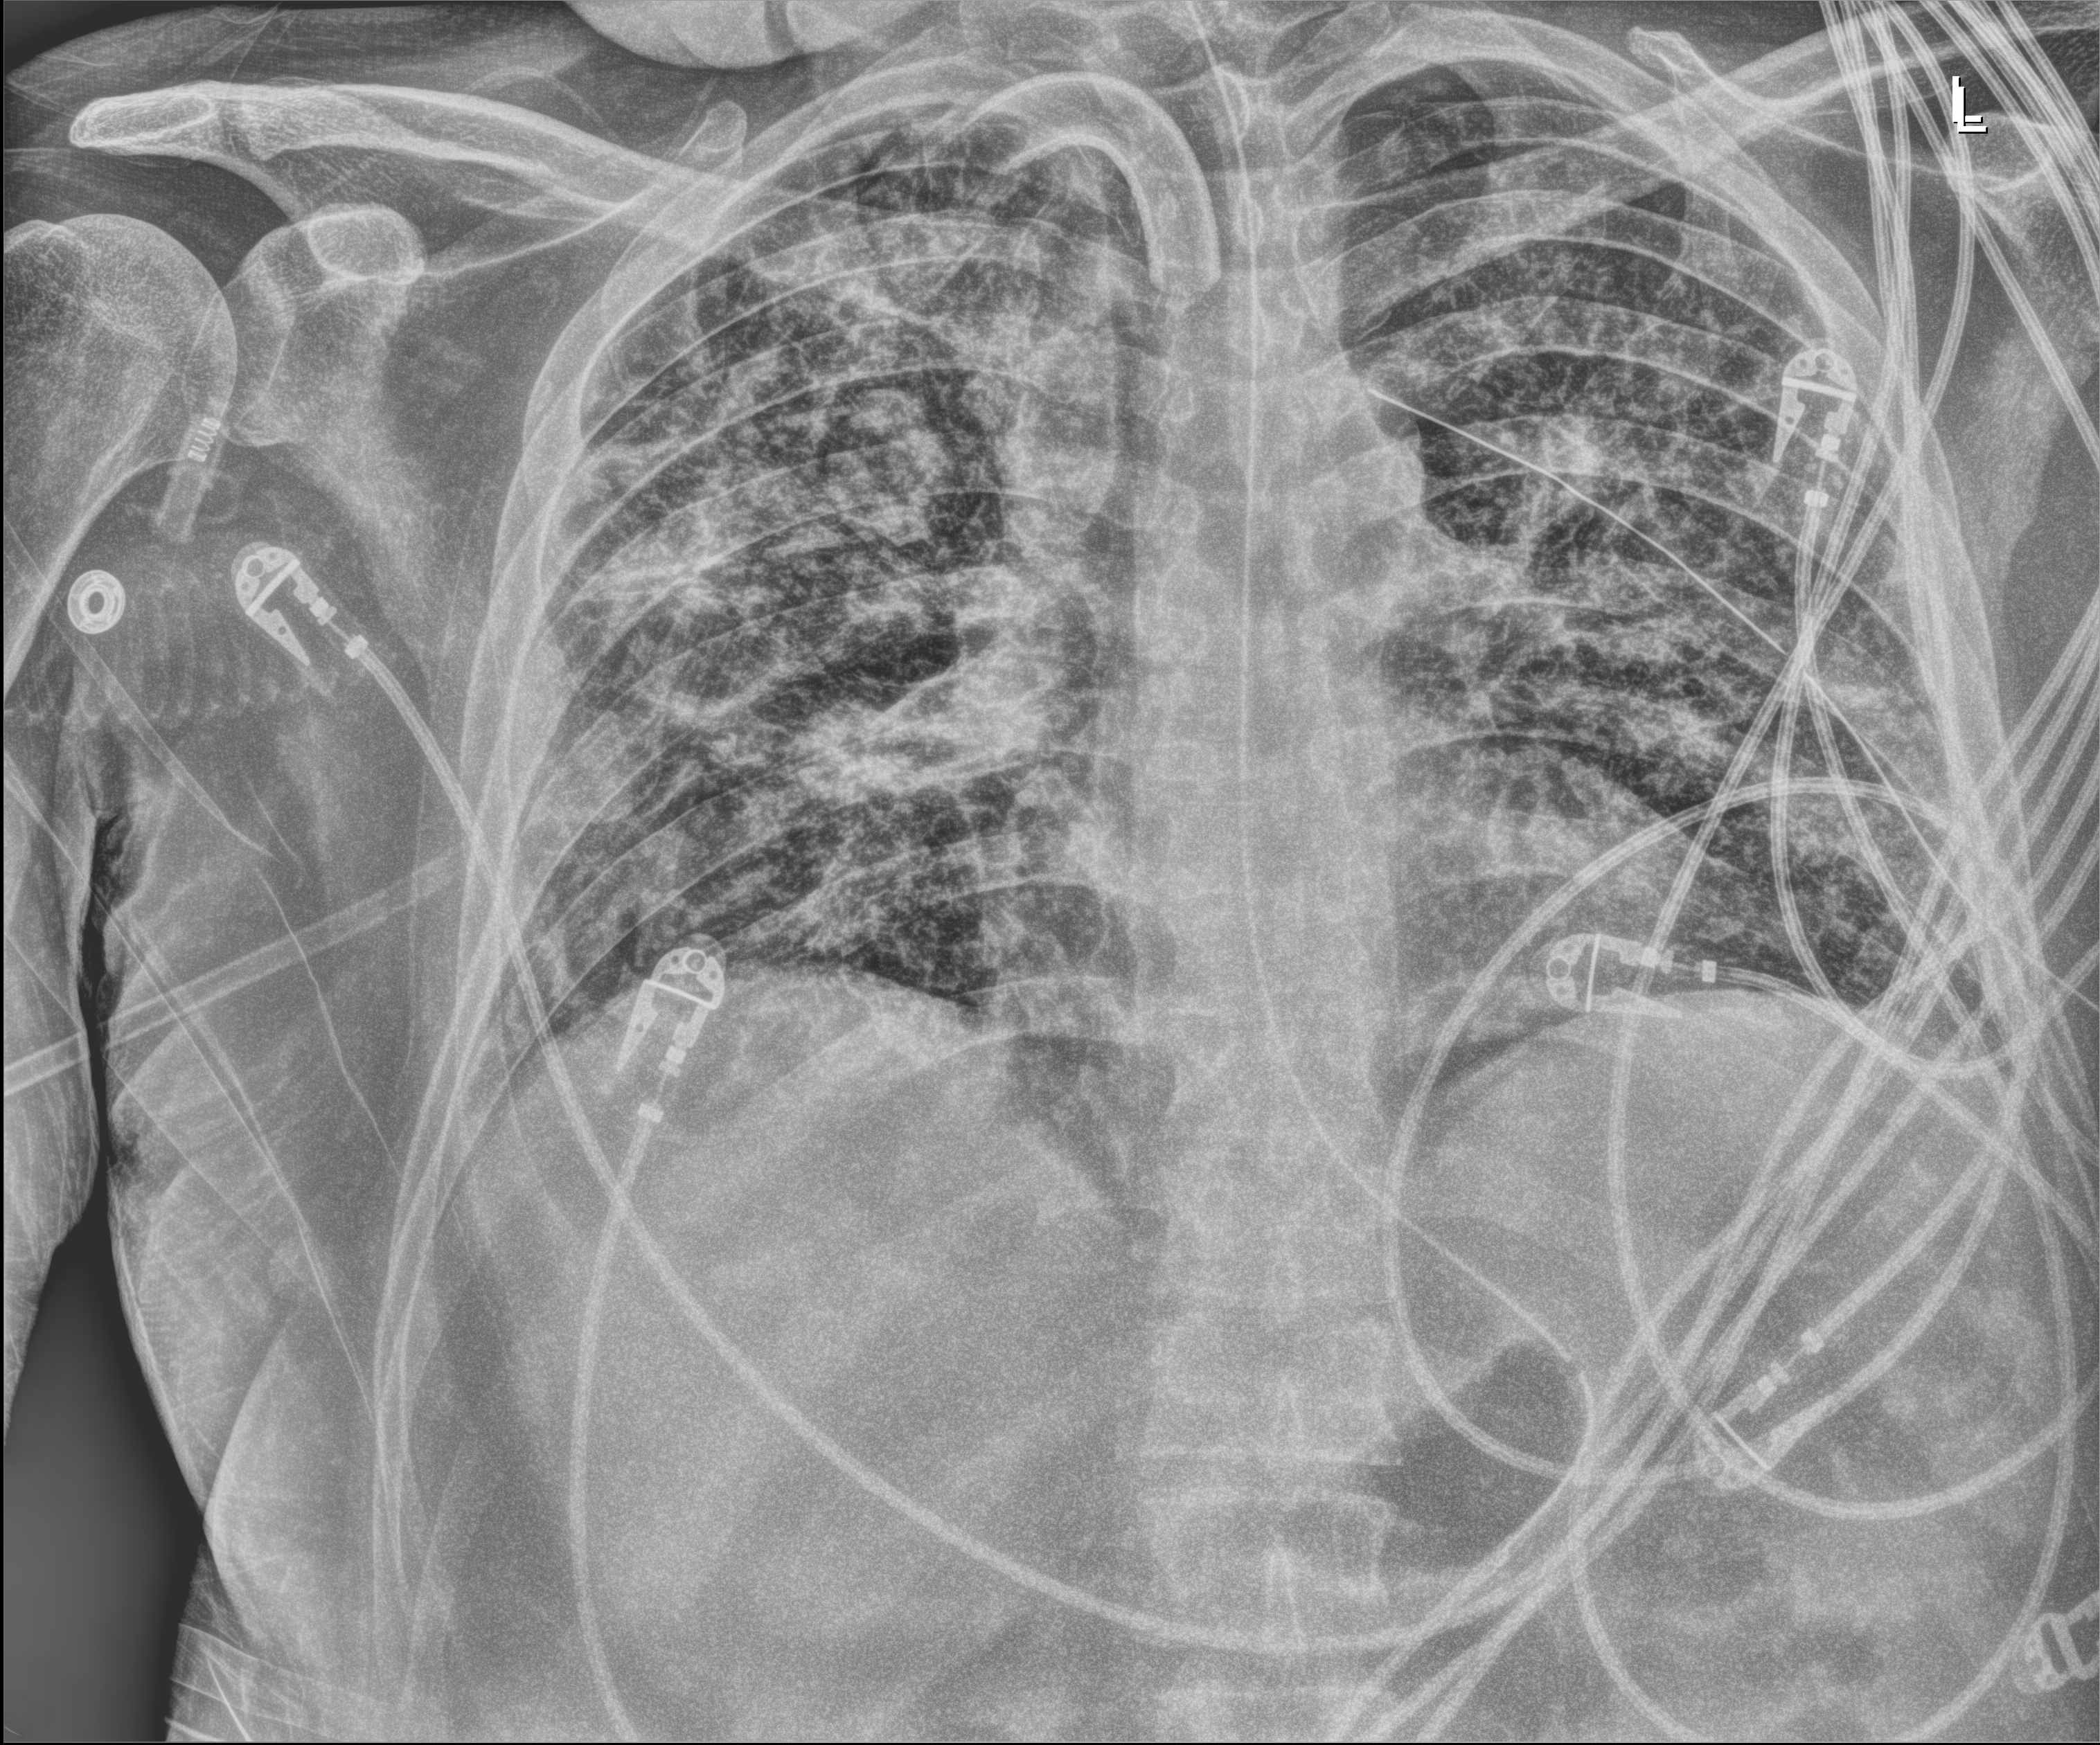
Portable chest radiograph; anteroposterior (AP) projection. Male patient hospitalised with COVID-19, age 18–59 years.
From the hospital-stay record, not from the radiograph (when in the stay this image was taken is not recorded):
- mechanically ventilated during this hospital stay: yes